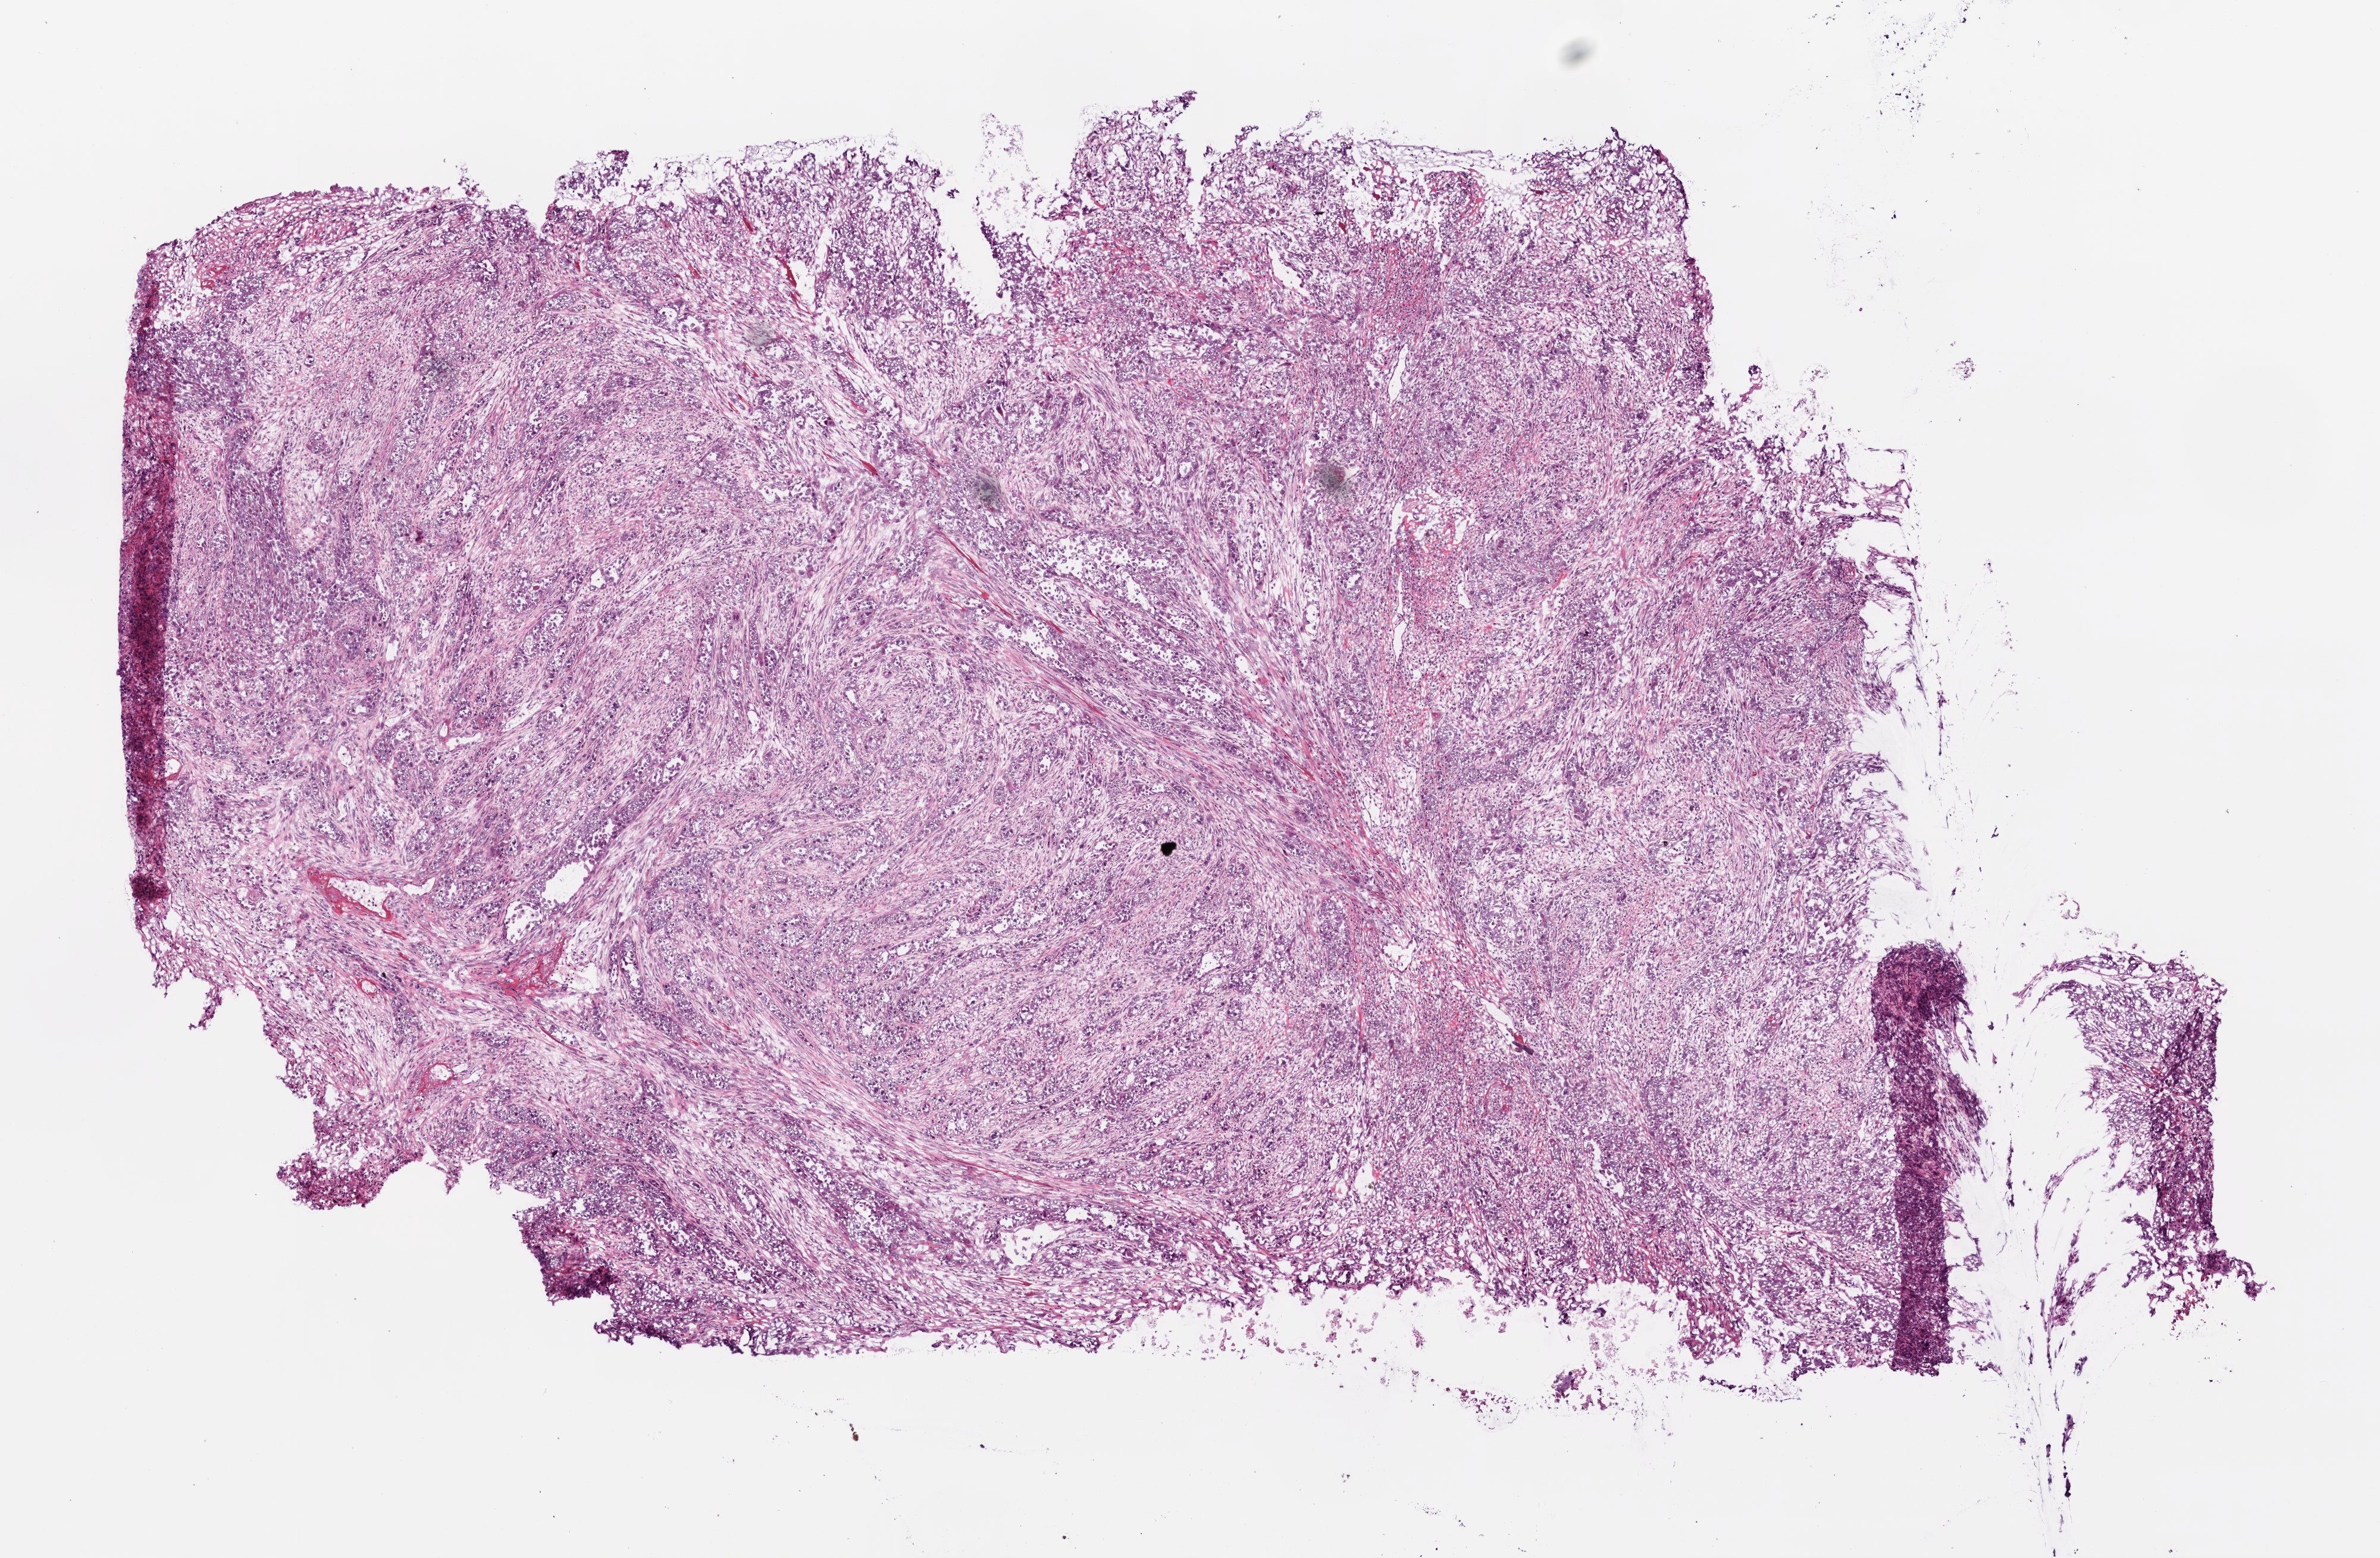
H&E-stained whole-slide image — shown as a low-resolution overview of the whole scanned area (about 8.0 x 5.3 mm, acquisition: 20x scan); frozen section from the top of the tissue portion; sample: primary tumour, head and neck. Male patient; age at initial diagnosis 69 years. Histologic grade: G3 (poorly differentiated). Slide review estimates, as recorded: tumour cells 89%, tumour nuclei 80%, normal cells 0%, stromal cells 10%, necrosis 1%.
• AJCC pathologic stage: IVA (6th edition)
• pathologic diagnosis: Squamous cell carcinoma, NOS